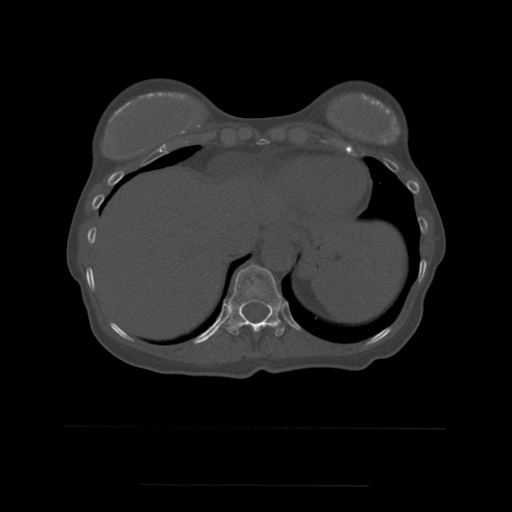
CT including the spine, one axial slice. Position 286 of 544 along the scan axis. Bone window (W 1800 / L 400 HU). 1.25 mm slice thickness. 512 × 512 image matrix. Patient age 58 years. From the clinical record (not read from this slice): primary cancer: lung.
Annotated regions visible in this slice (semi-automatically segmented with operator editing):
- T11 vertebra: bounding box <226,265,285,336> (left, top, right, bottom; pixels)